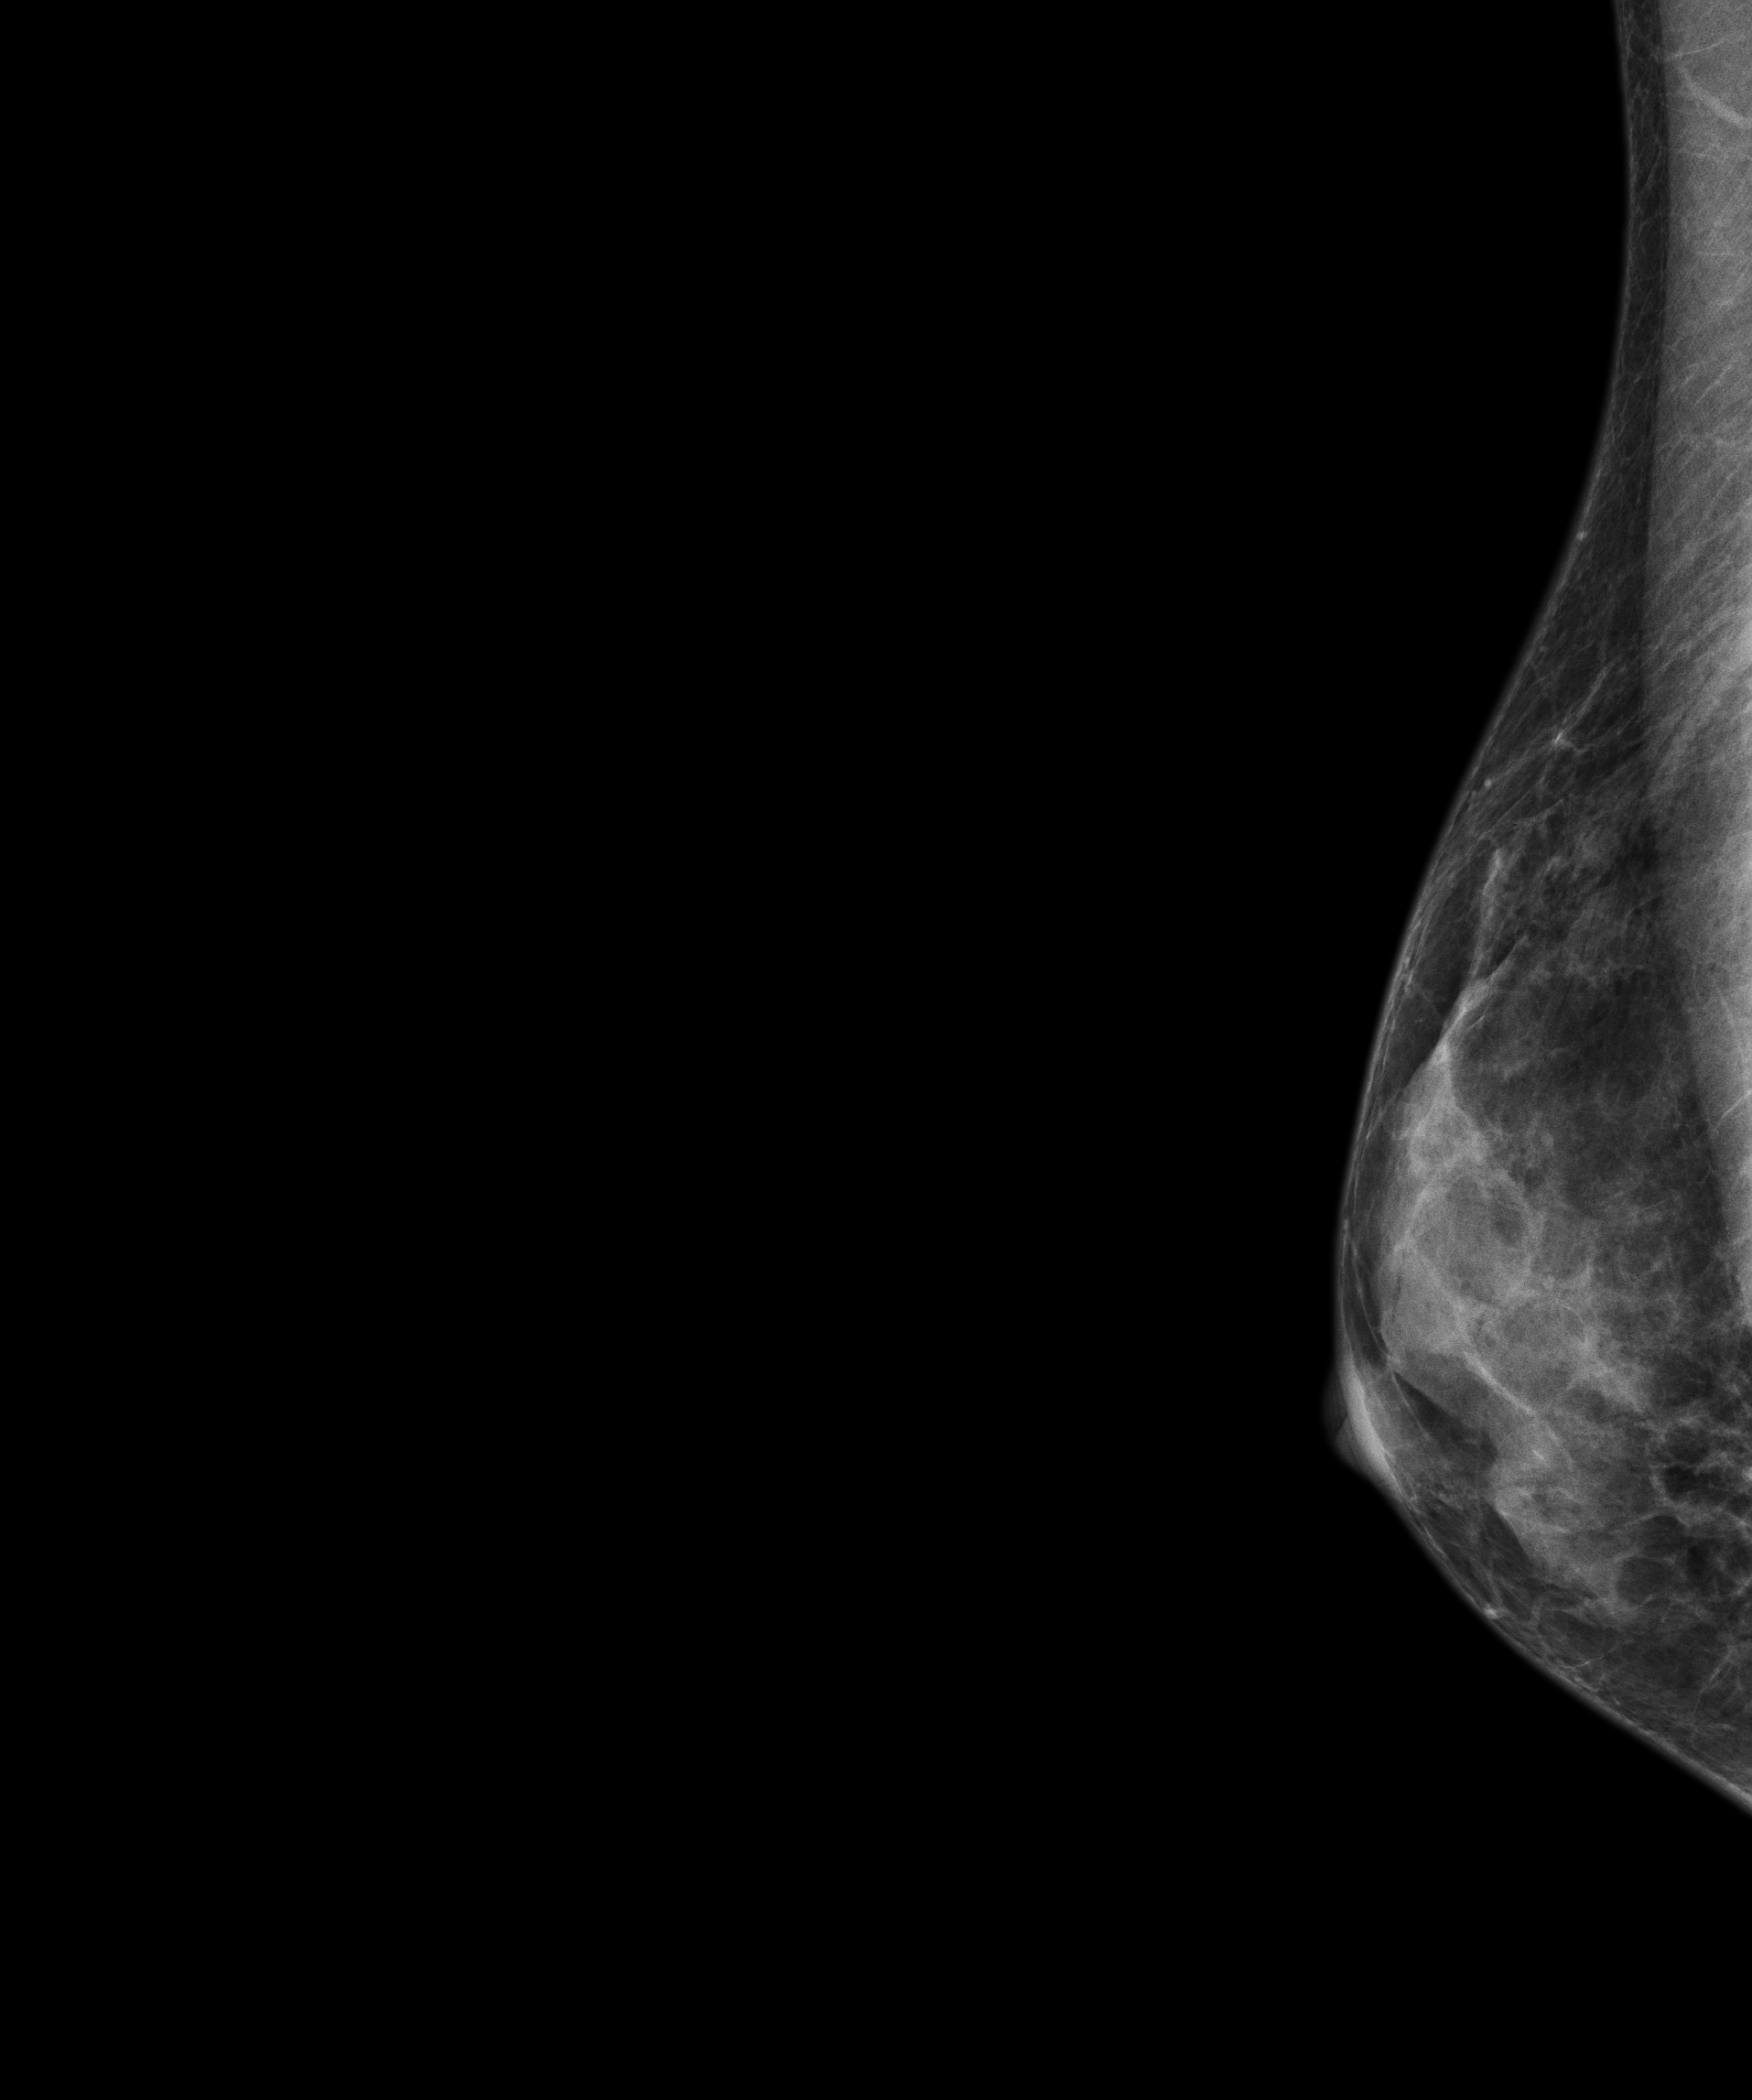
Annual screening mammography examination; compressed breast thickness 28 mm. Female patient, age 56 years.
Image type: full-field digital mammogram. Breast: right. Projection: exaggerated CC view (lateral).